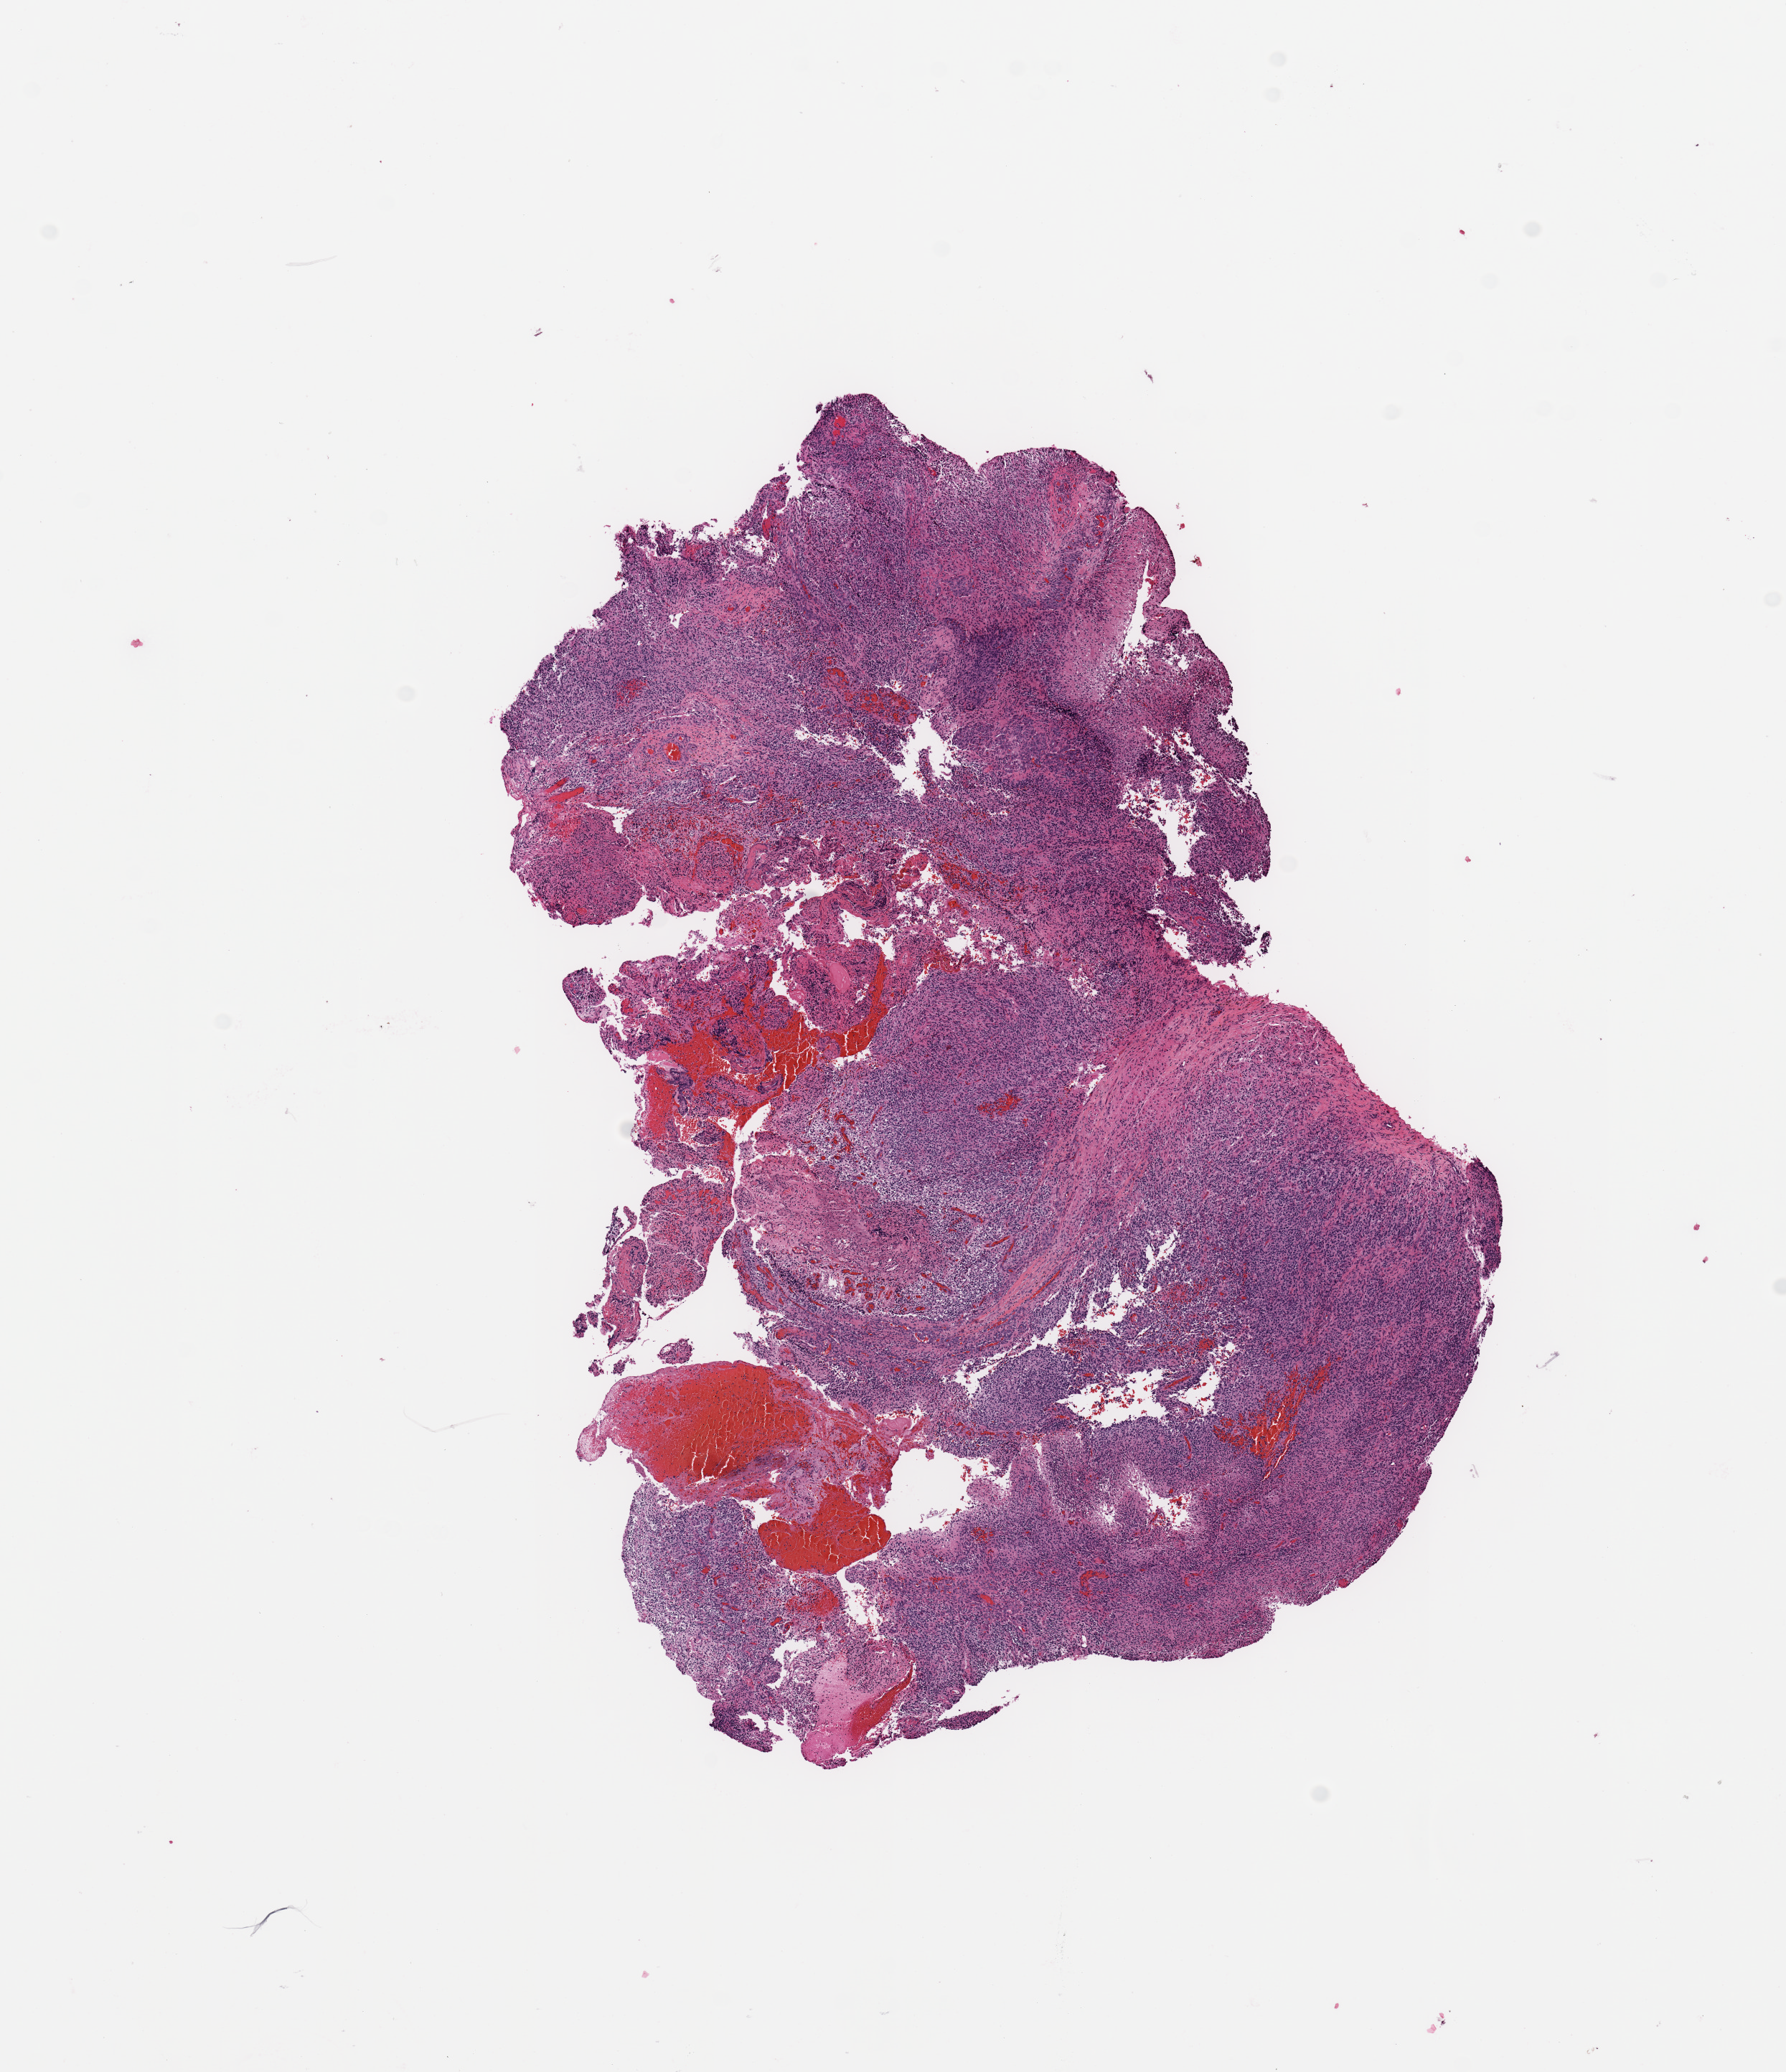
Whole-slide histology image, Hematoxylin and eosin (H&E) stained — whole scanned area (about 9.8 x 11.4 mm) shown as a low-resolution overview. Tumour tissue sample, sampled site: brain. 59-year-old male patient. Slide review estimates, as recorded: tumour nuclei 85%, necrosis 5%.
Histologic diagnosis: Glioblastoma.